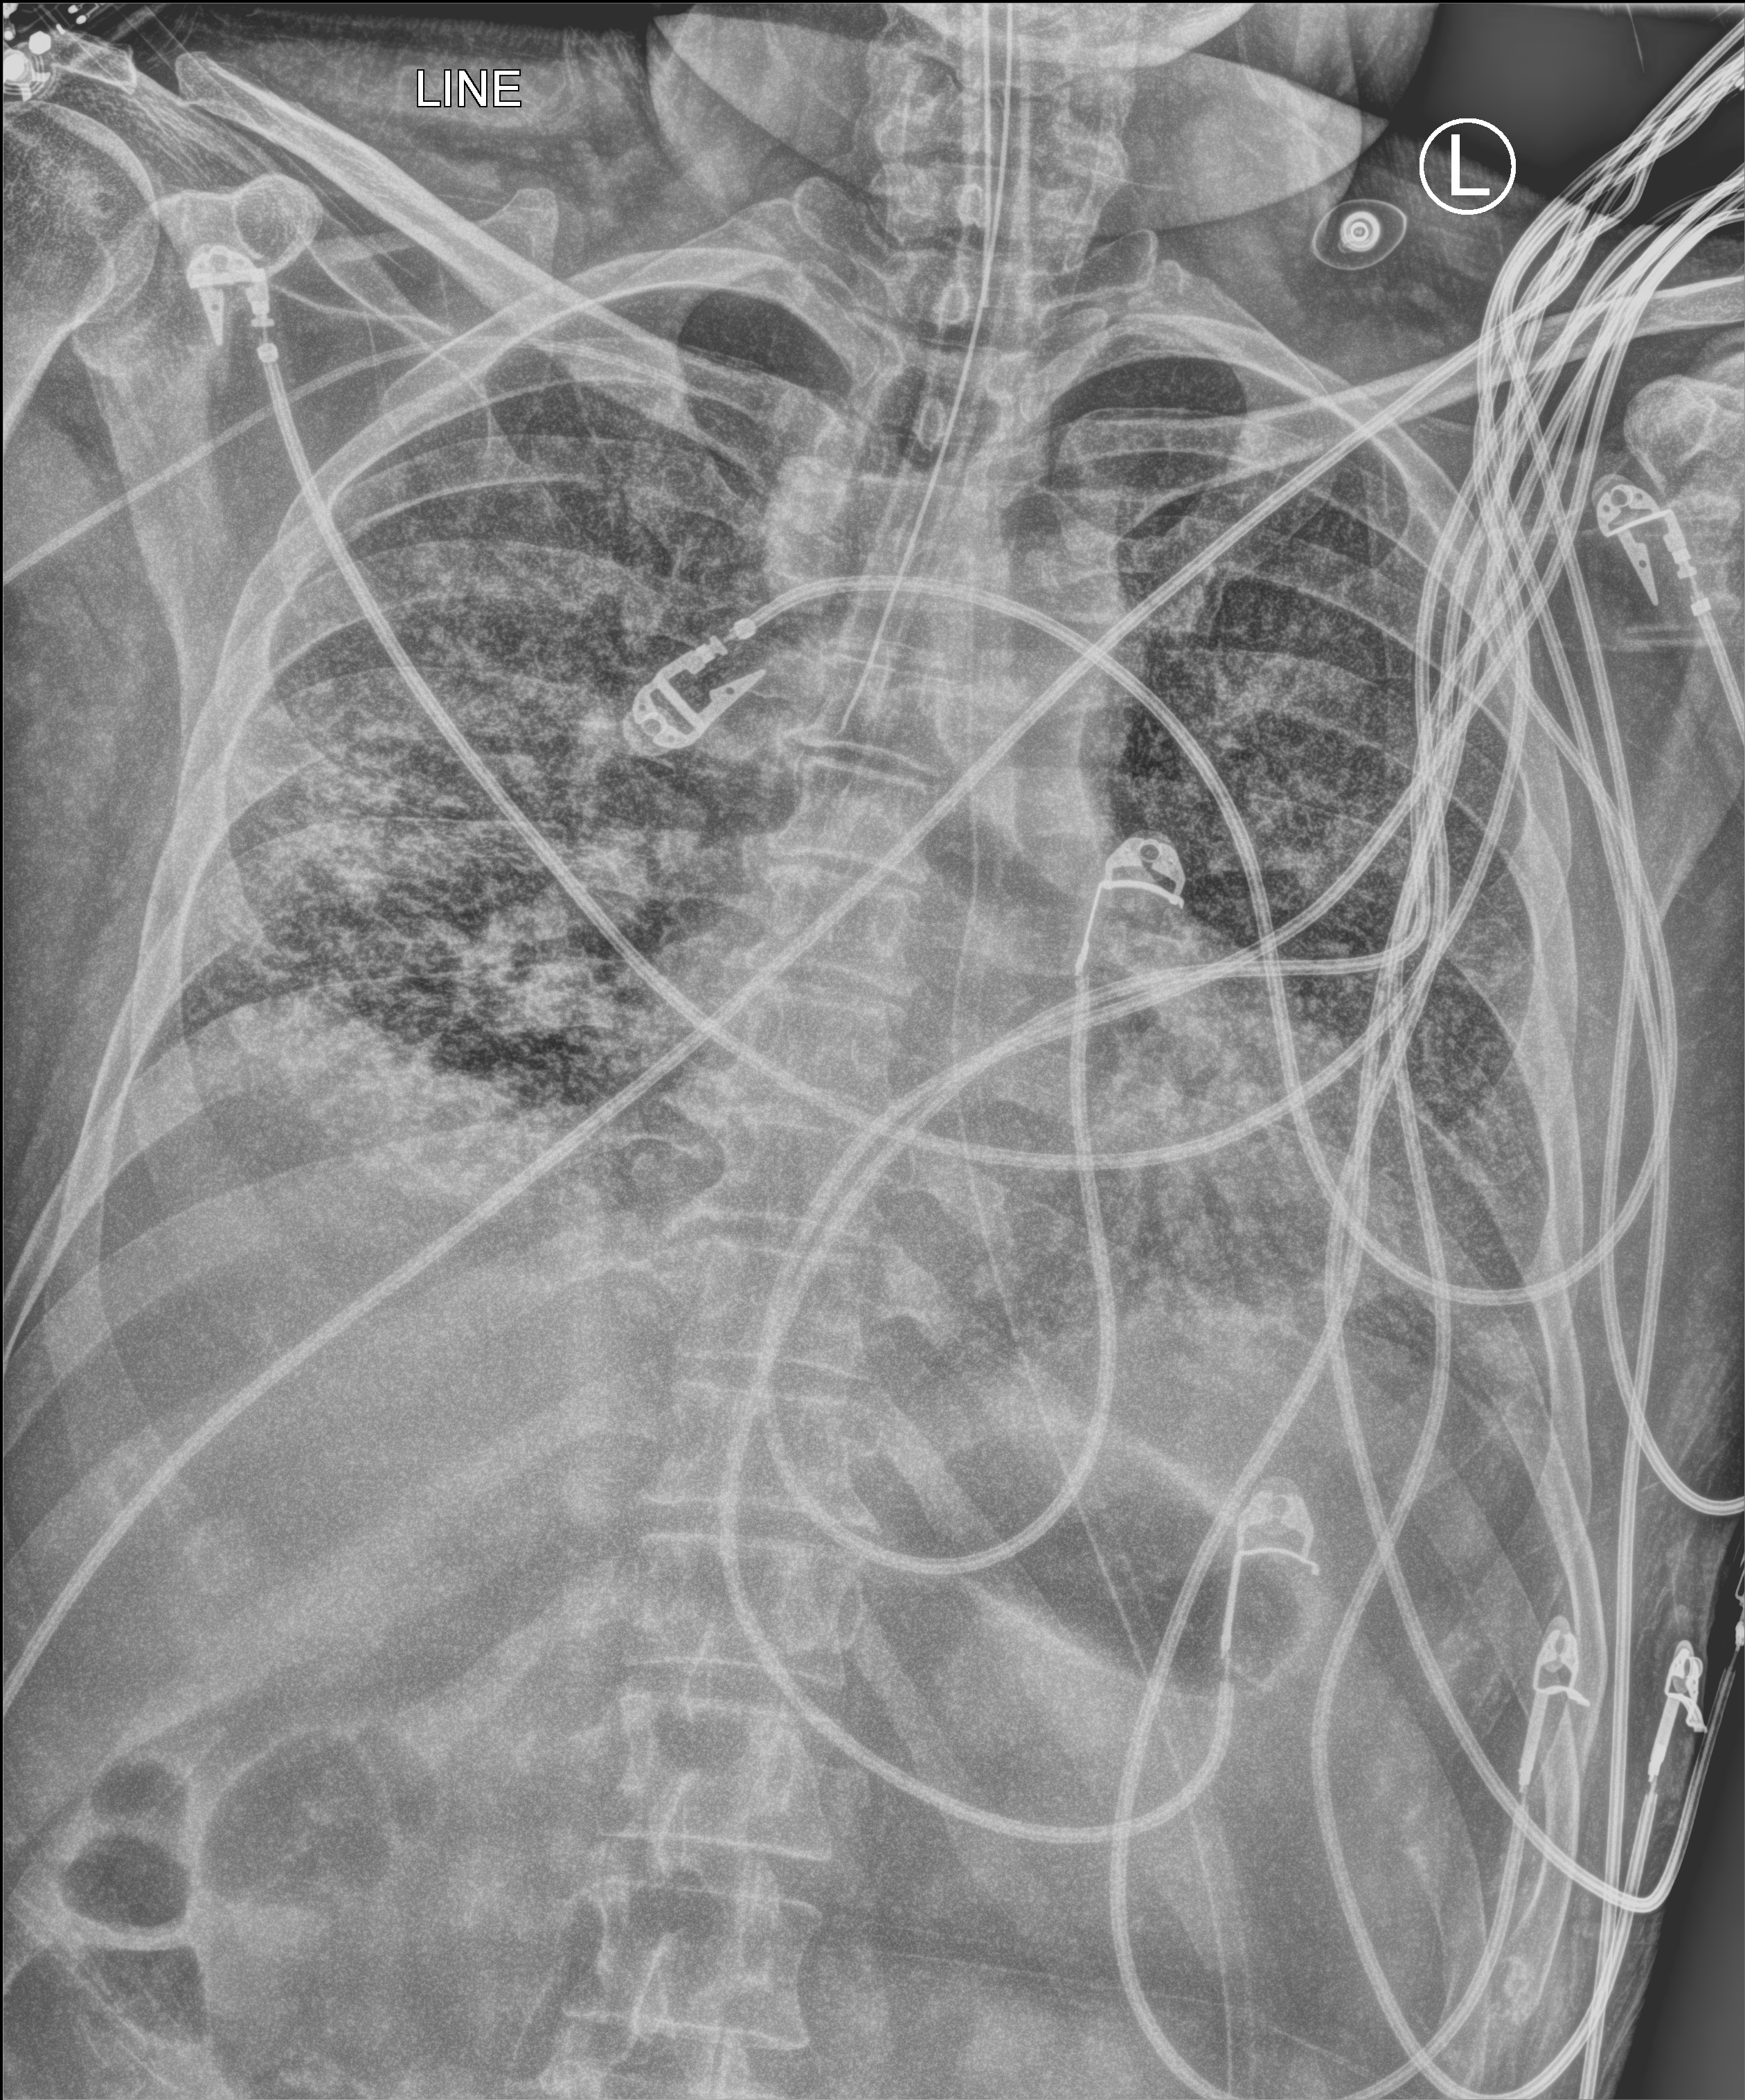
Portable chest radiograph, anteroposterior (AP) projection. Patient hospitalised with COVID-19; male, aged 18–59 years.
From the hospital-stay record, not from the radiograph (when in the stay this image was taken is not recorded):
- hypertension (admission record): no
- admitted to intensive care during this hospital stay: yes
- other chronic lung disease (admission record): no